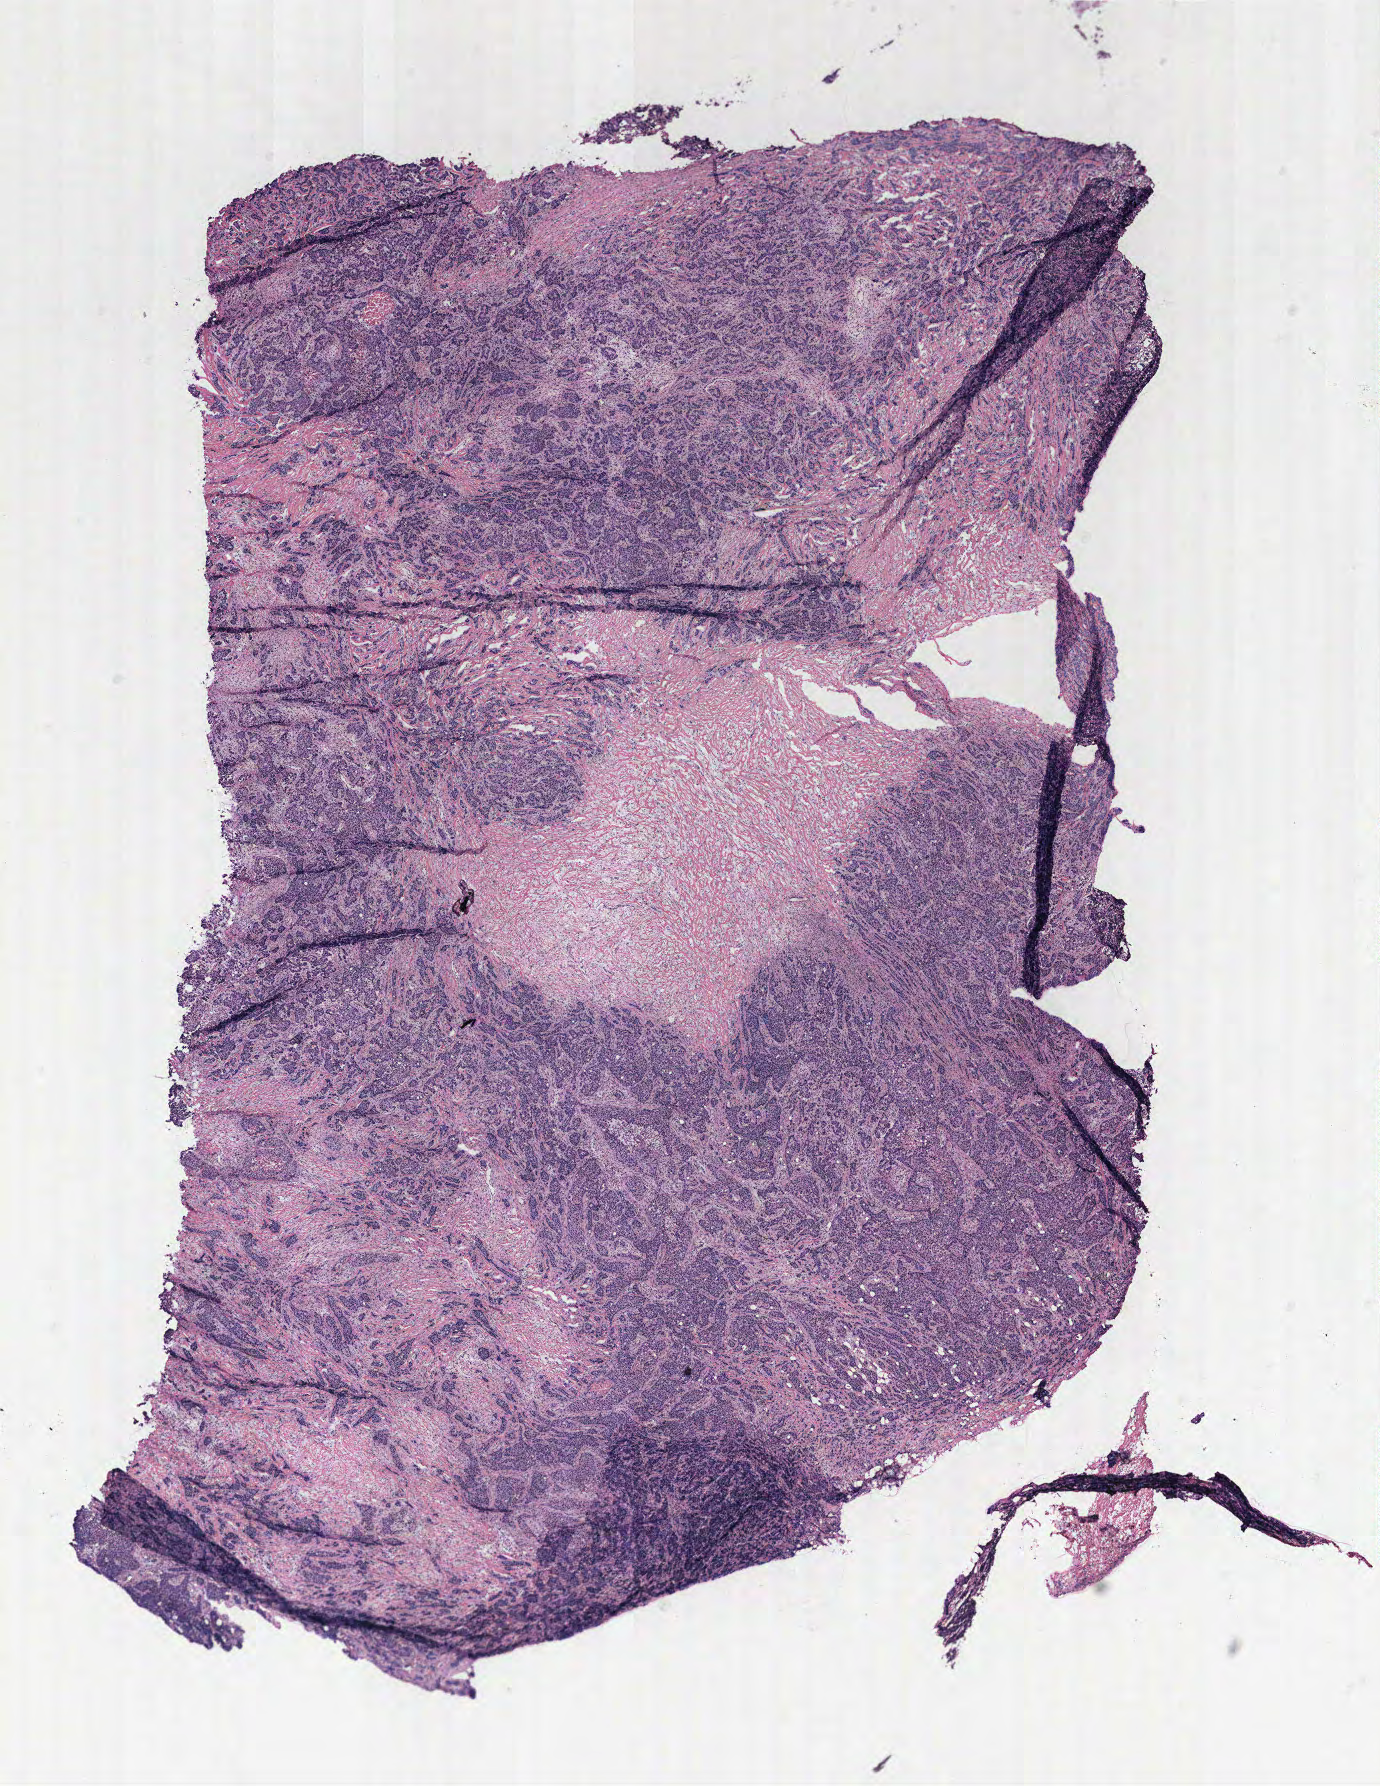
Whole-slide histology image, H&E, low-resolution overview of the scanned area, about 11.0 x 14.3 mm (from a 40x scan); breast, tumour tissue. 38-year-old female patient.
* AJCC pathologic stage: IIB
* diagnosis: Infiltrating duct carcinoma, NOS